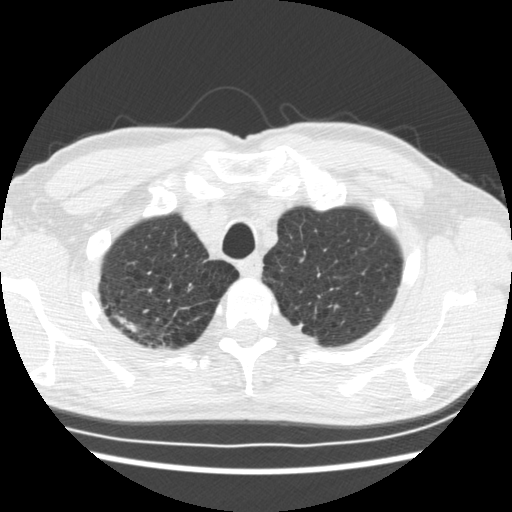
Low-dose screening chest CT, one axial slice. Slice 156 of 183 in the series (ordered by position). 120 kVp. Lung window (W 1500 / L -600 HU). 2.5 mm slice thickness. 512 × 512 image matrix, field of view 339 × 339 mm.
Structures marked on this image (outlined manually by an expert reader):
- lesion 1 (tumor, upper lobe of right lung): bounding box [x1, y1, x2, y2] px = [114, 314, 138, 333]